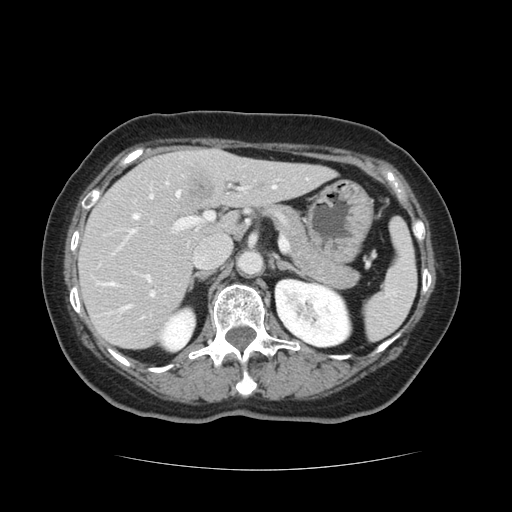
Contrast-enhanced abdominal CT, one axial slice. Slice 73 of 128 in the series (ordered by position). 120 kVp. Intravenous contrast given. Soft-tissue window (W 400 / L 40 HU). 512 × 512 image matrix. Female patient, age 67 years. Case-level facts recorded for this patient, not image findings: diagnosis: colorectal cancer liver metastases, imaged before liver resection.
Outlined on this slice (manually delineated by an expert):
- hepatic veins: bounding box [x1, y1, x2, y2] px = [102, 186, 276, 310]
- liver: [79, 148, 329, 349]
- planned liver remnant (the part of the liver to remain after resection): [79, 160, 328, 349]
- portal vein (with intrahepatic branches): [119, 187, 248, 297]
- liver metastasis: [189, 182, 217, 198]